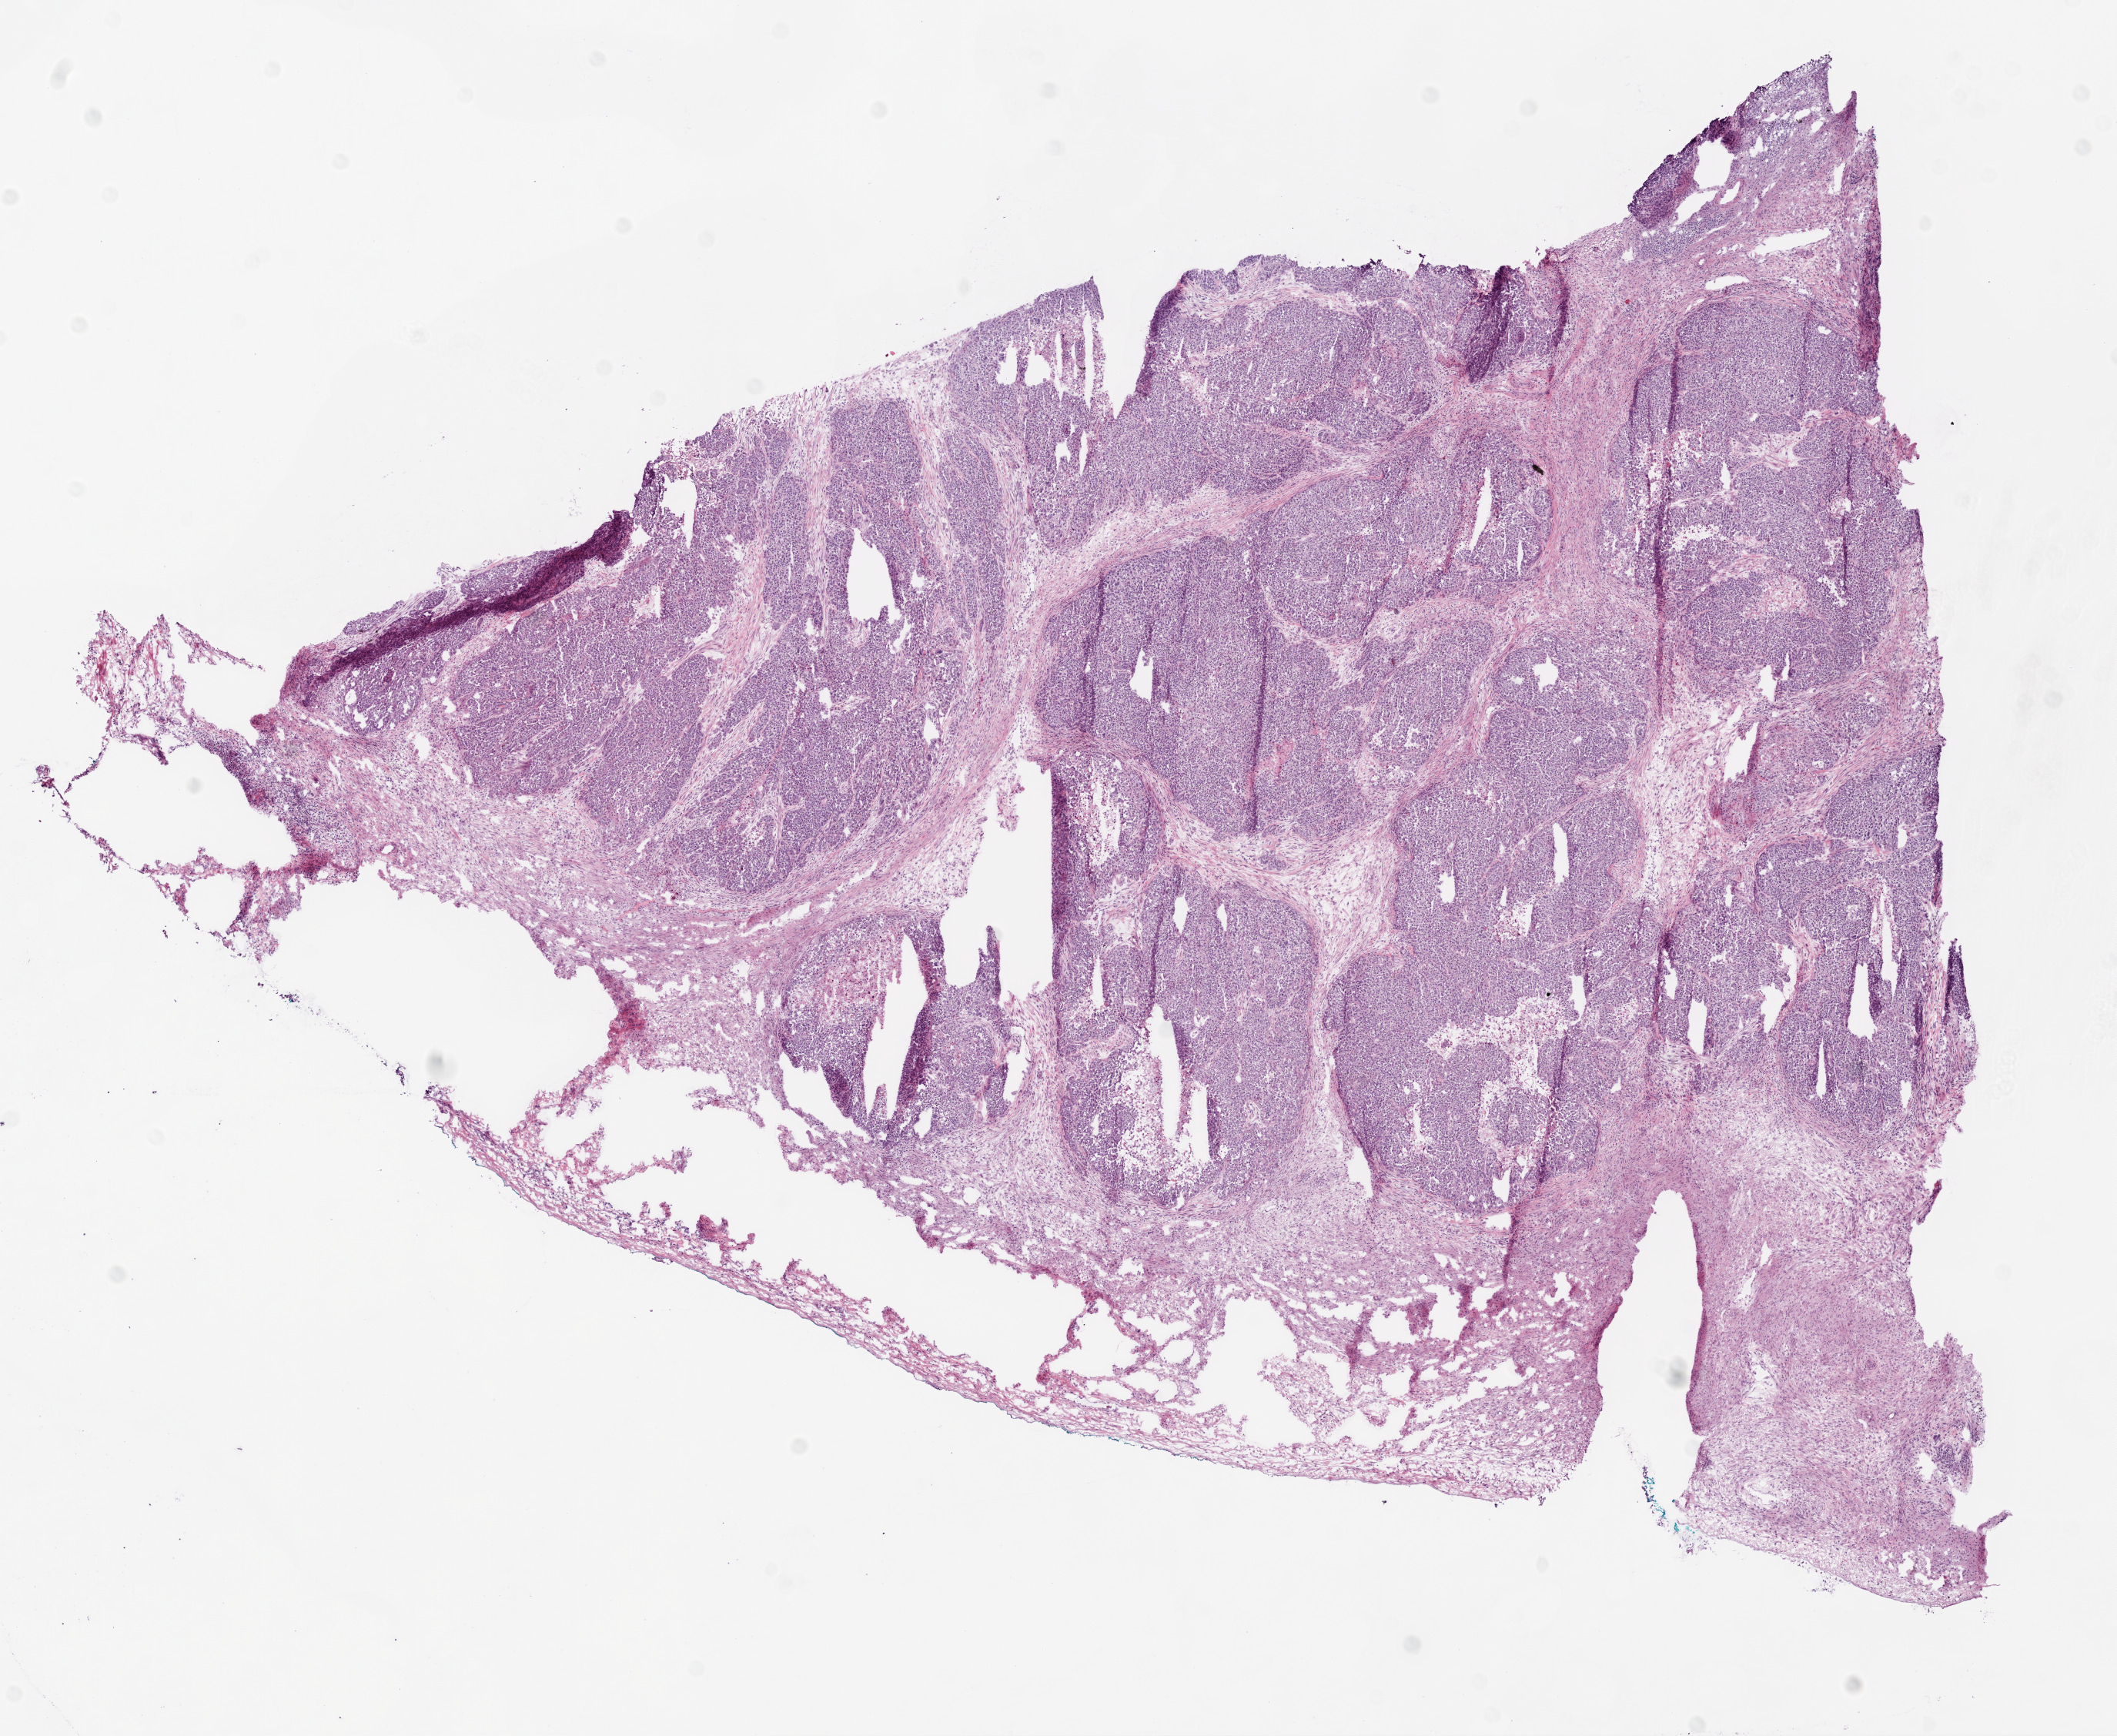
H&E whole-slide image — shown as a low-resolution overview of the whole scanned area (about 11.0 x 9.0 mm), frozen section, sample: primary tumour, ovary. Female, age 47 years at initial diagnosis. Histologic grade: G3 (poorly differentiated). Composition of this section per pathologist review: tumour cells 70%, tumour nuclei 95%, normal cells 0%, stromal cells 27%, necrosis 3%.
* diagnosis: Serous cystadenocarcinoma, NOS
* laterality: bilateral
* FIGO stage: IIIC